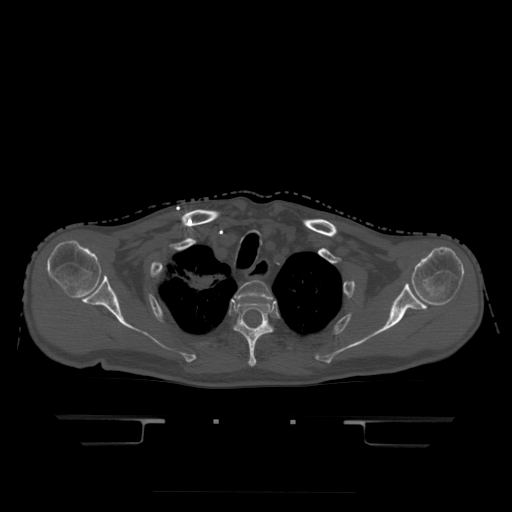
CT including the spine, one axial slice; position 373 of 522 along the scan axis; bone window (W 1800 / L 400 HU); 1.25 mm slice thickness; 512 × 512 image matrix, field of view 436 × 436 mm. Patient age 68 years. Case-level facts recorded for this patient, not image findings: primary cancer: urothelial.
Annotated regions visible in this slice (semi-automatic segmentation, software-assisted and operator-edited):
- T2 vertebra: box from (x=235, y=281) to (x=273, y=300) px
- T3 vertebra: (x=235, y=299)–(x=273, y=367)